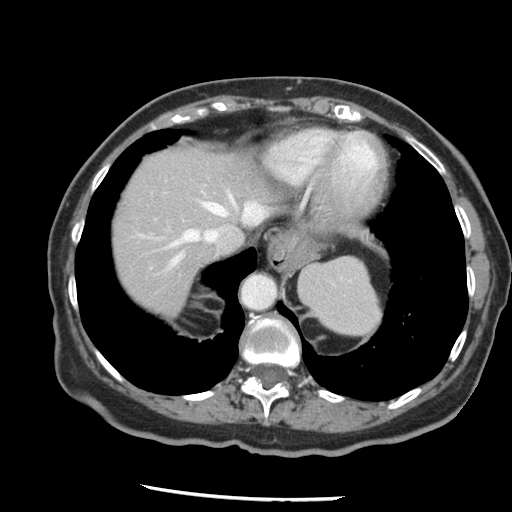
Contrast-enhanced abdominal CT, one axial slice; reconstruction kernel STANDARD; soft-tissue window (W 400 / L 40 HU); 2.5 mm slice thickness; 512 × 512 image matrix, field of view 330 × 330 mm. Female patient, age 85 years. From the clinical record (not read from this slice): diagnosis: colorectal cancer liver metastases, imaged before liver resection.
Annotated regions visible in this slice (outlined manually by an expert reader):
- hepatic veins: bounding box (x1, y1, x2, y2) in pixels: (170, 195, 263, 266)
- liver: (111, 145, 282, 317)
- planned liver remnant (the part of the liver to remain after resection): (111, 145, 282, 317)